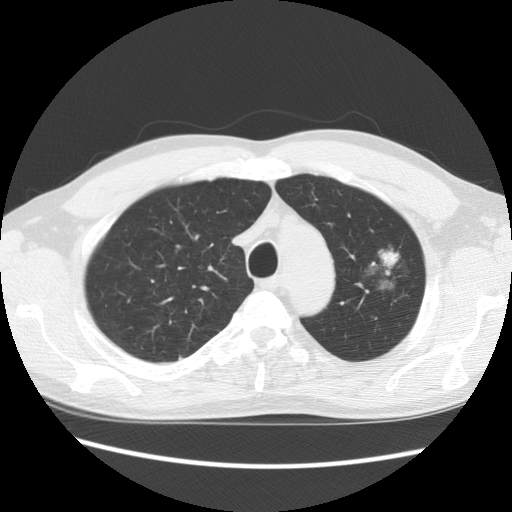
Axial slice from a low-dose chest CT screening exam. Second annual screen. Lung window (W 1500 / L -600 HU). 2.5 mm slice thickness. Standard (soft-tissue) reconstruction kernel (STANDARD). 140 kVp. Male, age 61 years at enrolment. Former smoker at enrolment.
- Expert reader's lesion annotation, bounding box (x1, y1, x2, y2) in pixels: (343, 223, 427, 302).
- Reader record for this screening exam (exam-level; its link to the box is not recorded): non-calcified nodule or mass ≥4 mm, left upper lobe, 34 × 32 mm, poorly defined margins, mixed attenuation, pre-existing on the prior screen: yes; interval growth: no.
- Participant outcome: lung cancer diagnosed 704 days after this screen — bronchiolo-alveolar adenocarcinoma, NOS, left upper lobe, well differentiated (G1), stage IB (AJCC 6th edition), 44 mm at pathology.